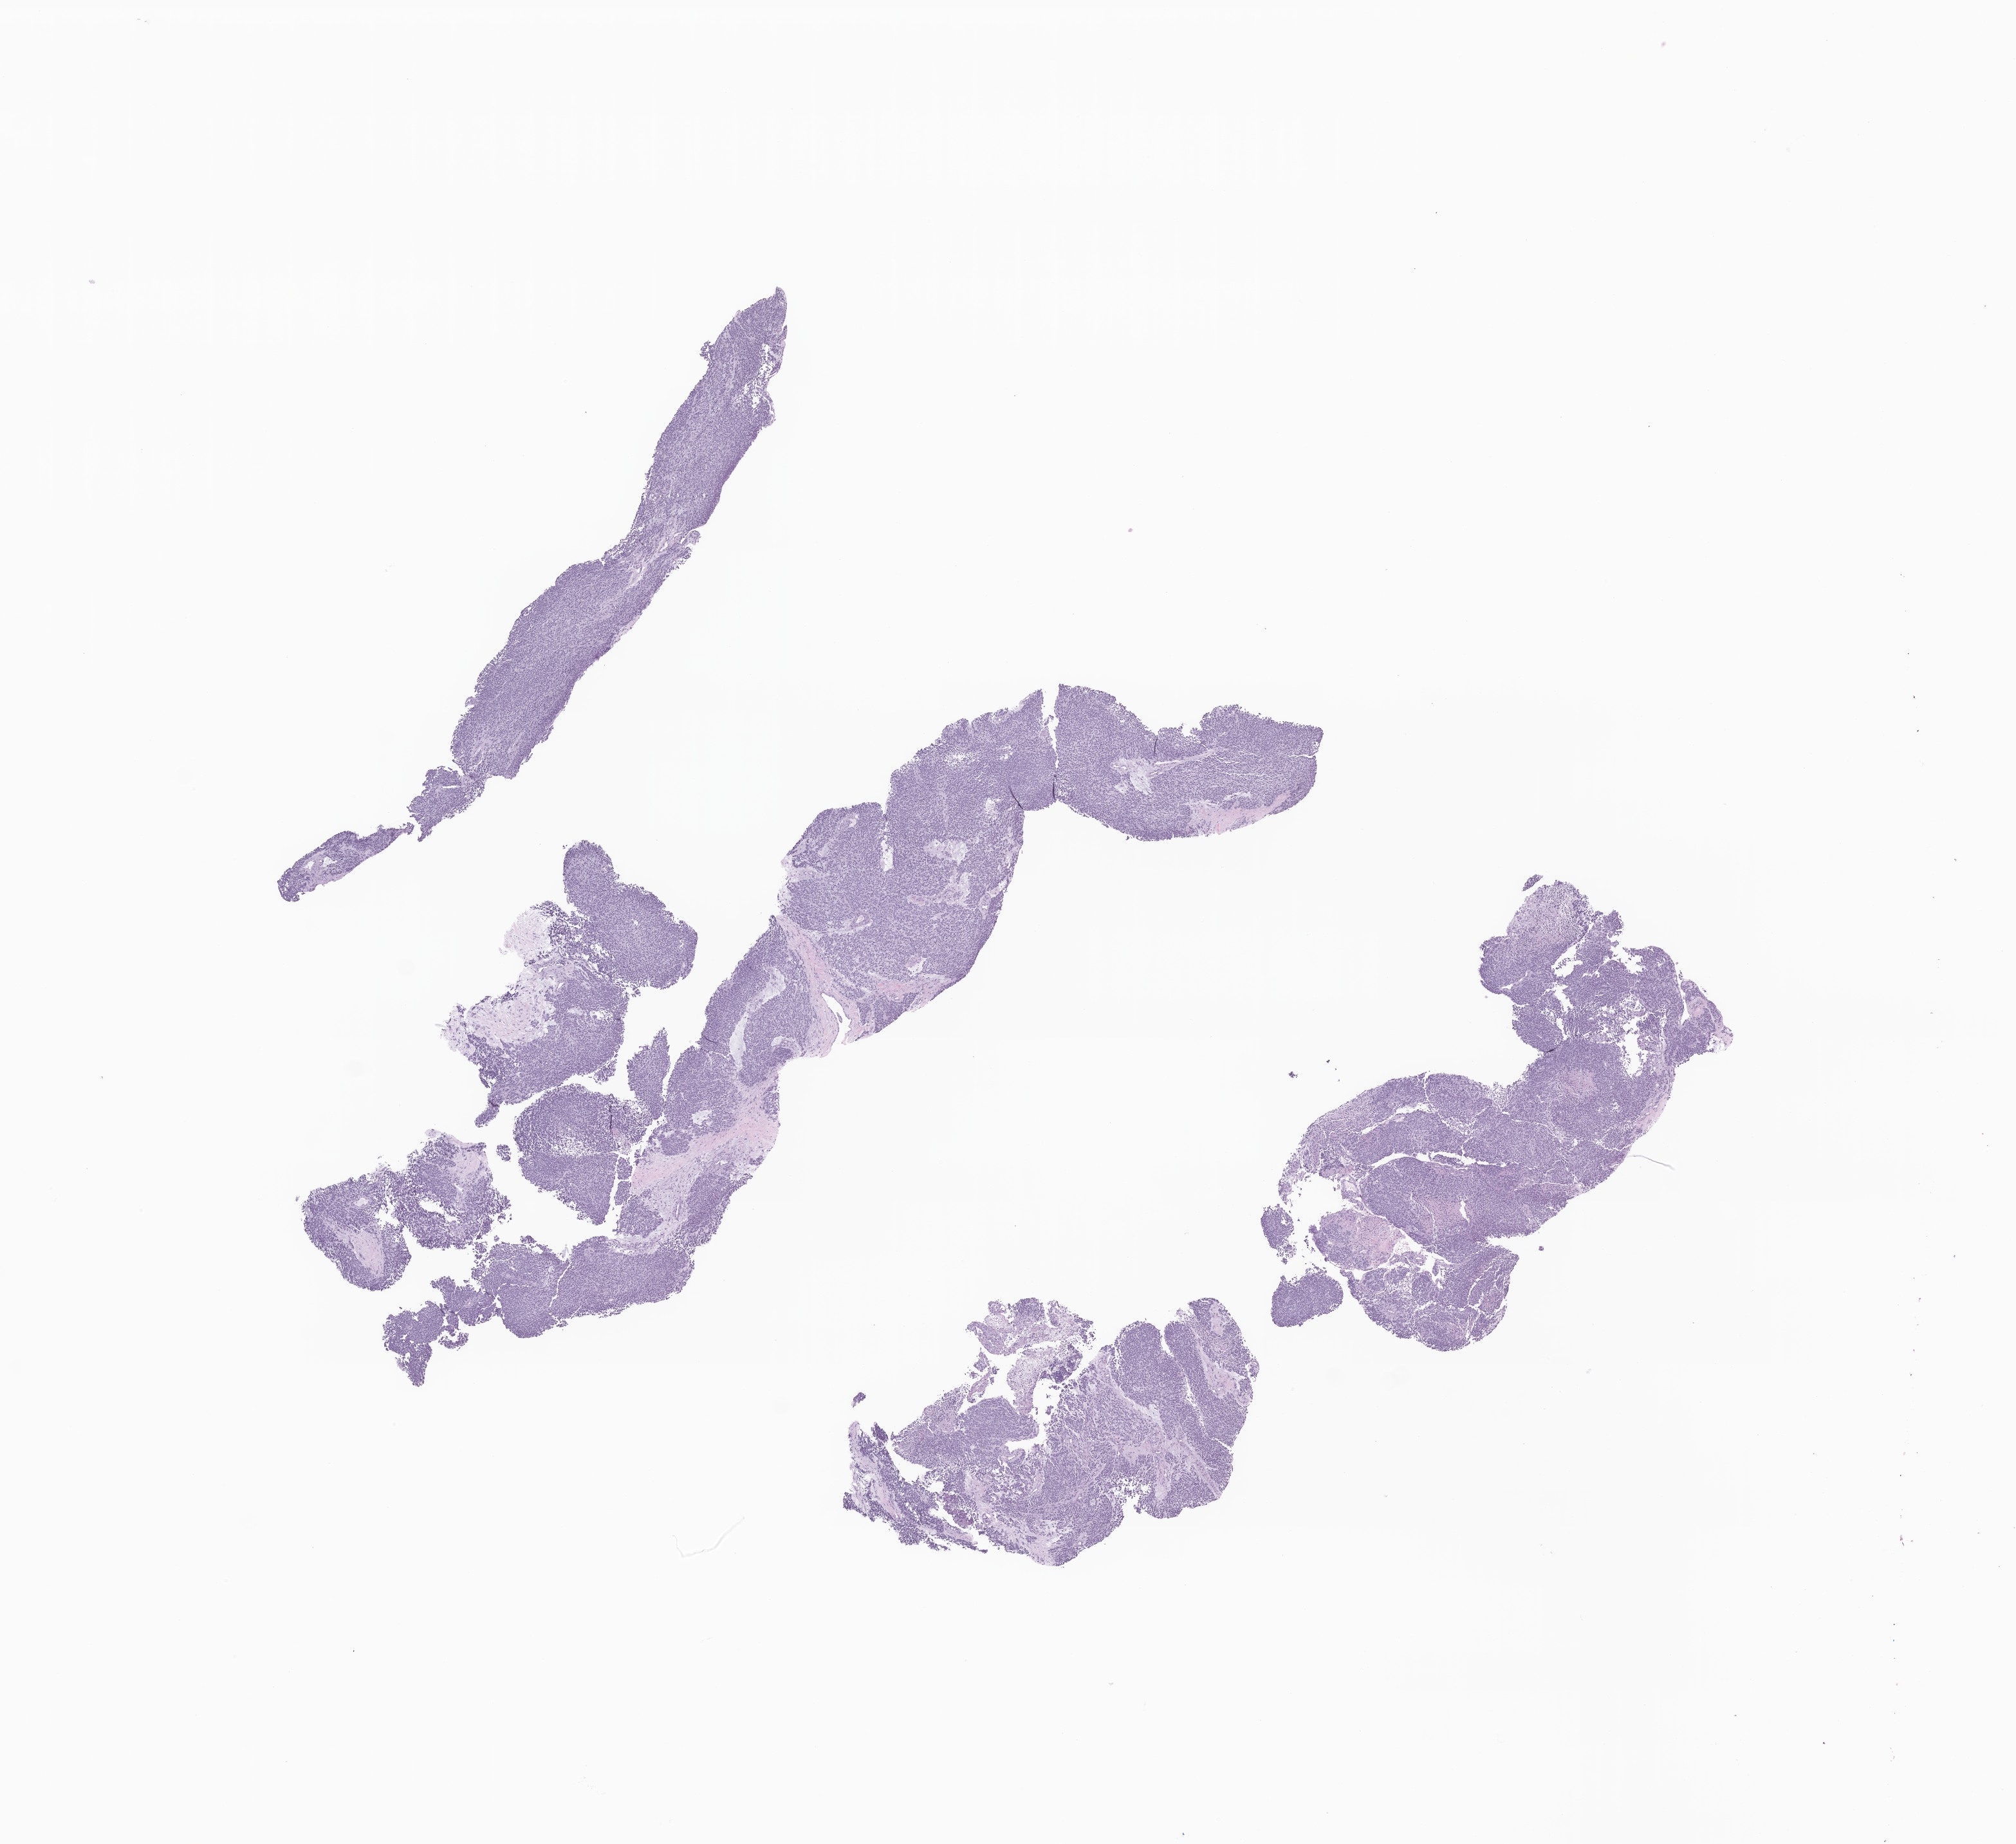
Hematoxylin and eosin (H&E) whole-slide image of tumor tissue from the retroperitoneum — a low-resolution overview of the entire scanned area, about 13.2 x 12.1 mm; FFPE section. Patient female; age 130 months (10 years 10 months).
Diagnosis: Neuroblastoma, NOS.